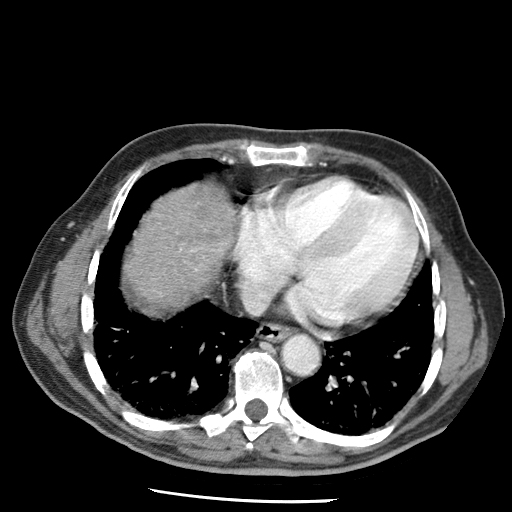
Contrast-enhanced abdominal CT (liver protocol), one axial slice; position 65 of 79 along the scan axis; reconstruction kernel STANDARD; soft-tissue window (W 400 / L 40 HU); 2.5 mm slice thickness; 512 × 512 image matrix. Case-level facts recorded for this patient, not image findings: diagnosis: hepatocellular carcinoma (patient treated with transarterial chemoembolisation; whether this scan precedes or follows treatment is not stated here); TNM stage (as recorded): Stage-IIIA; Child-Pugh class: A; tumour differentiation: moderately differentiated; tumour size: 7 cm.
Outlined on this slice (semi-automatically segmented with operator editing):
- liver parenchyma outside the tumour (the mass and vessels are separate outlines, so this box may not span the whole liver): bounding box (x1, y1, x2, y2) in pixels: (124, 184, 236, 308)
- liver vessels: (180, 250, 197, 270)